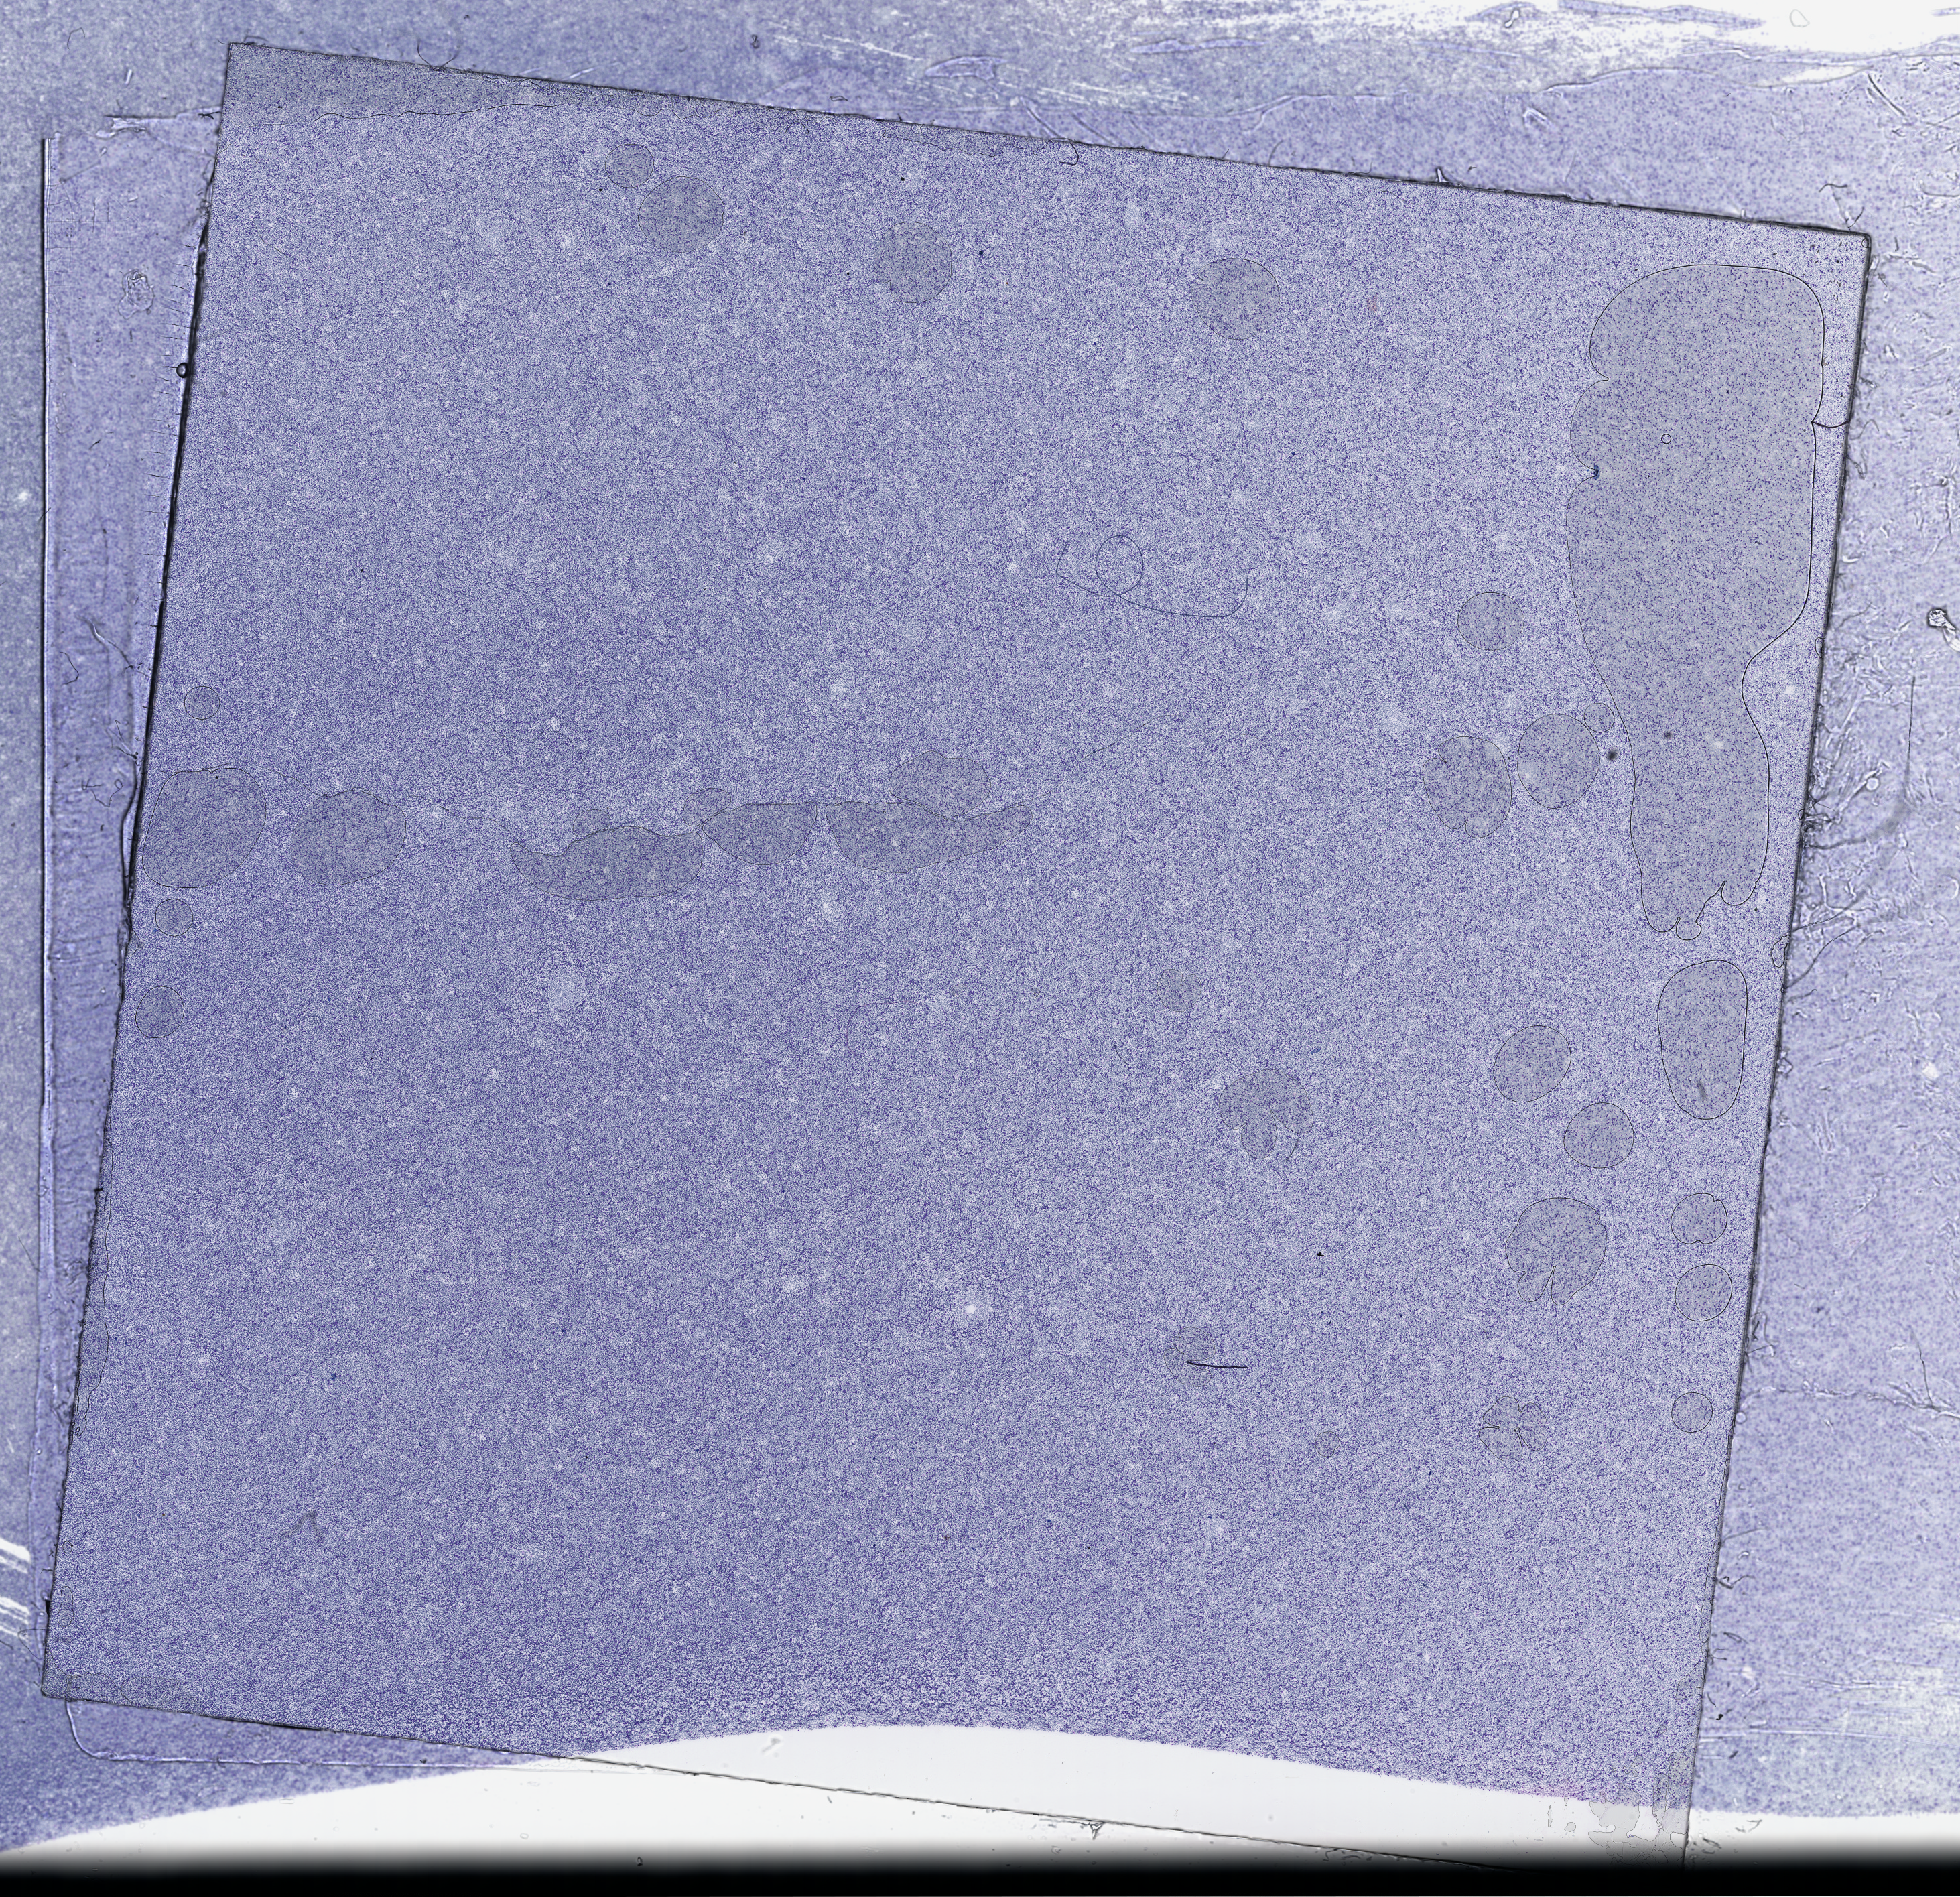
H&E-stained whole-slide image, a low-resolution overview of the entire scanned area, about 23.6 x 22.9 mm; peripheral blood (leukaemic) sample. Patient: female, age 80 years.
Diagnosis: Acute Myeloid Leukemia. WHO classification: AML with minimal differentiation.